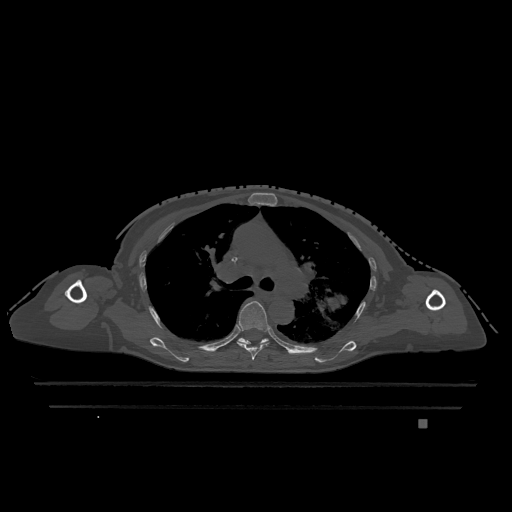
CT including the spine, one axial slice; position 821 of 1317 along the scan axis; bone window (W 1800 / L 400 HU); 0.5 mm slice thickness; 512 × 512 image matrix. Female patient, age 74 years. Case-level facts recorded for this patient, not image findings: primary cancer: lung; vertebrae with lytic lesions (as recorded): T1, T4, T5, T6, L4, L5.
Structures marked on this image (semi-automatic segmentation, software-assisted and operator-edited):
- T5 vertebra: bounding box (x1, y1, x2, y2) in pixels: (237, 301, 269, 360)
- T6 vertebra: (238, 338, 269, 344)